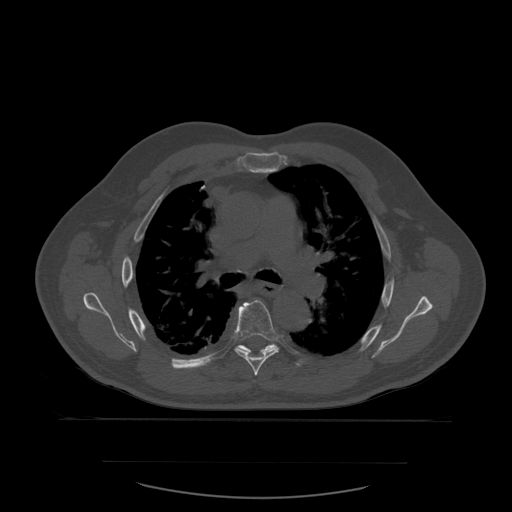
CT including the spine, one axial slice. Slice 400 of 590 in the series (ordered by position). Bone window (W 1800 / L 400 HU). 1.25 mm slice thickness. 512 × 512 image matrix. Patient age 71 years. From the clinical record (not read from this slice): primary cancer: lung.
Outlined on this slice (semi-automatic segmentation, software-assisted and operator-edited):
- T6 vertebra: bounding box [x1, y1, x2, y2] px = [235, 300, 280, 376]
- T7 vertebra: [237, 344, 276, 353]